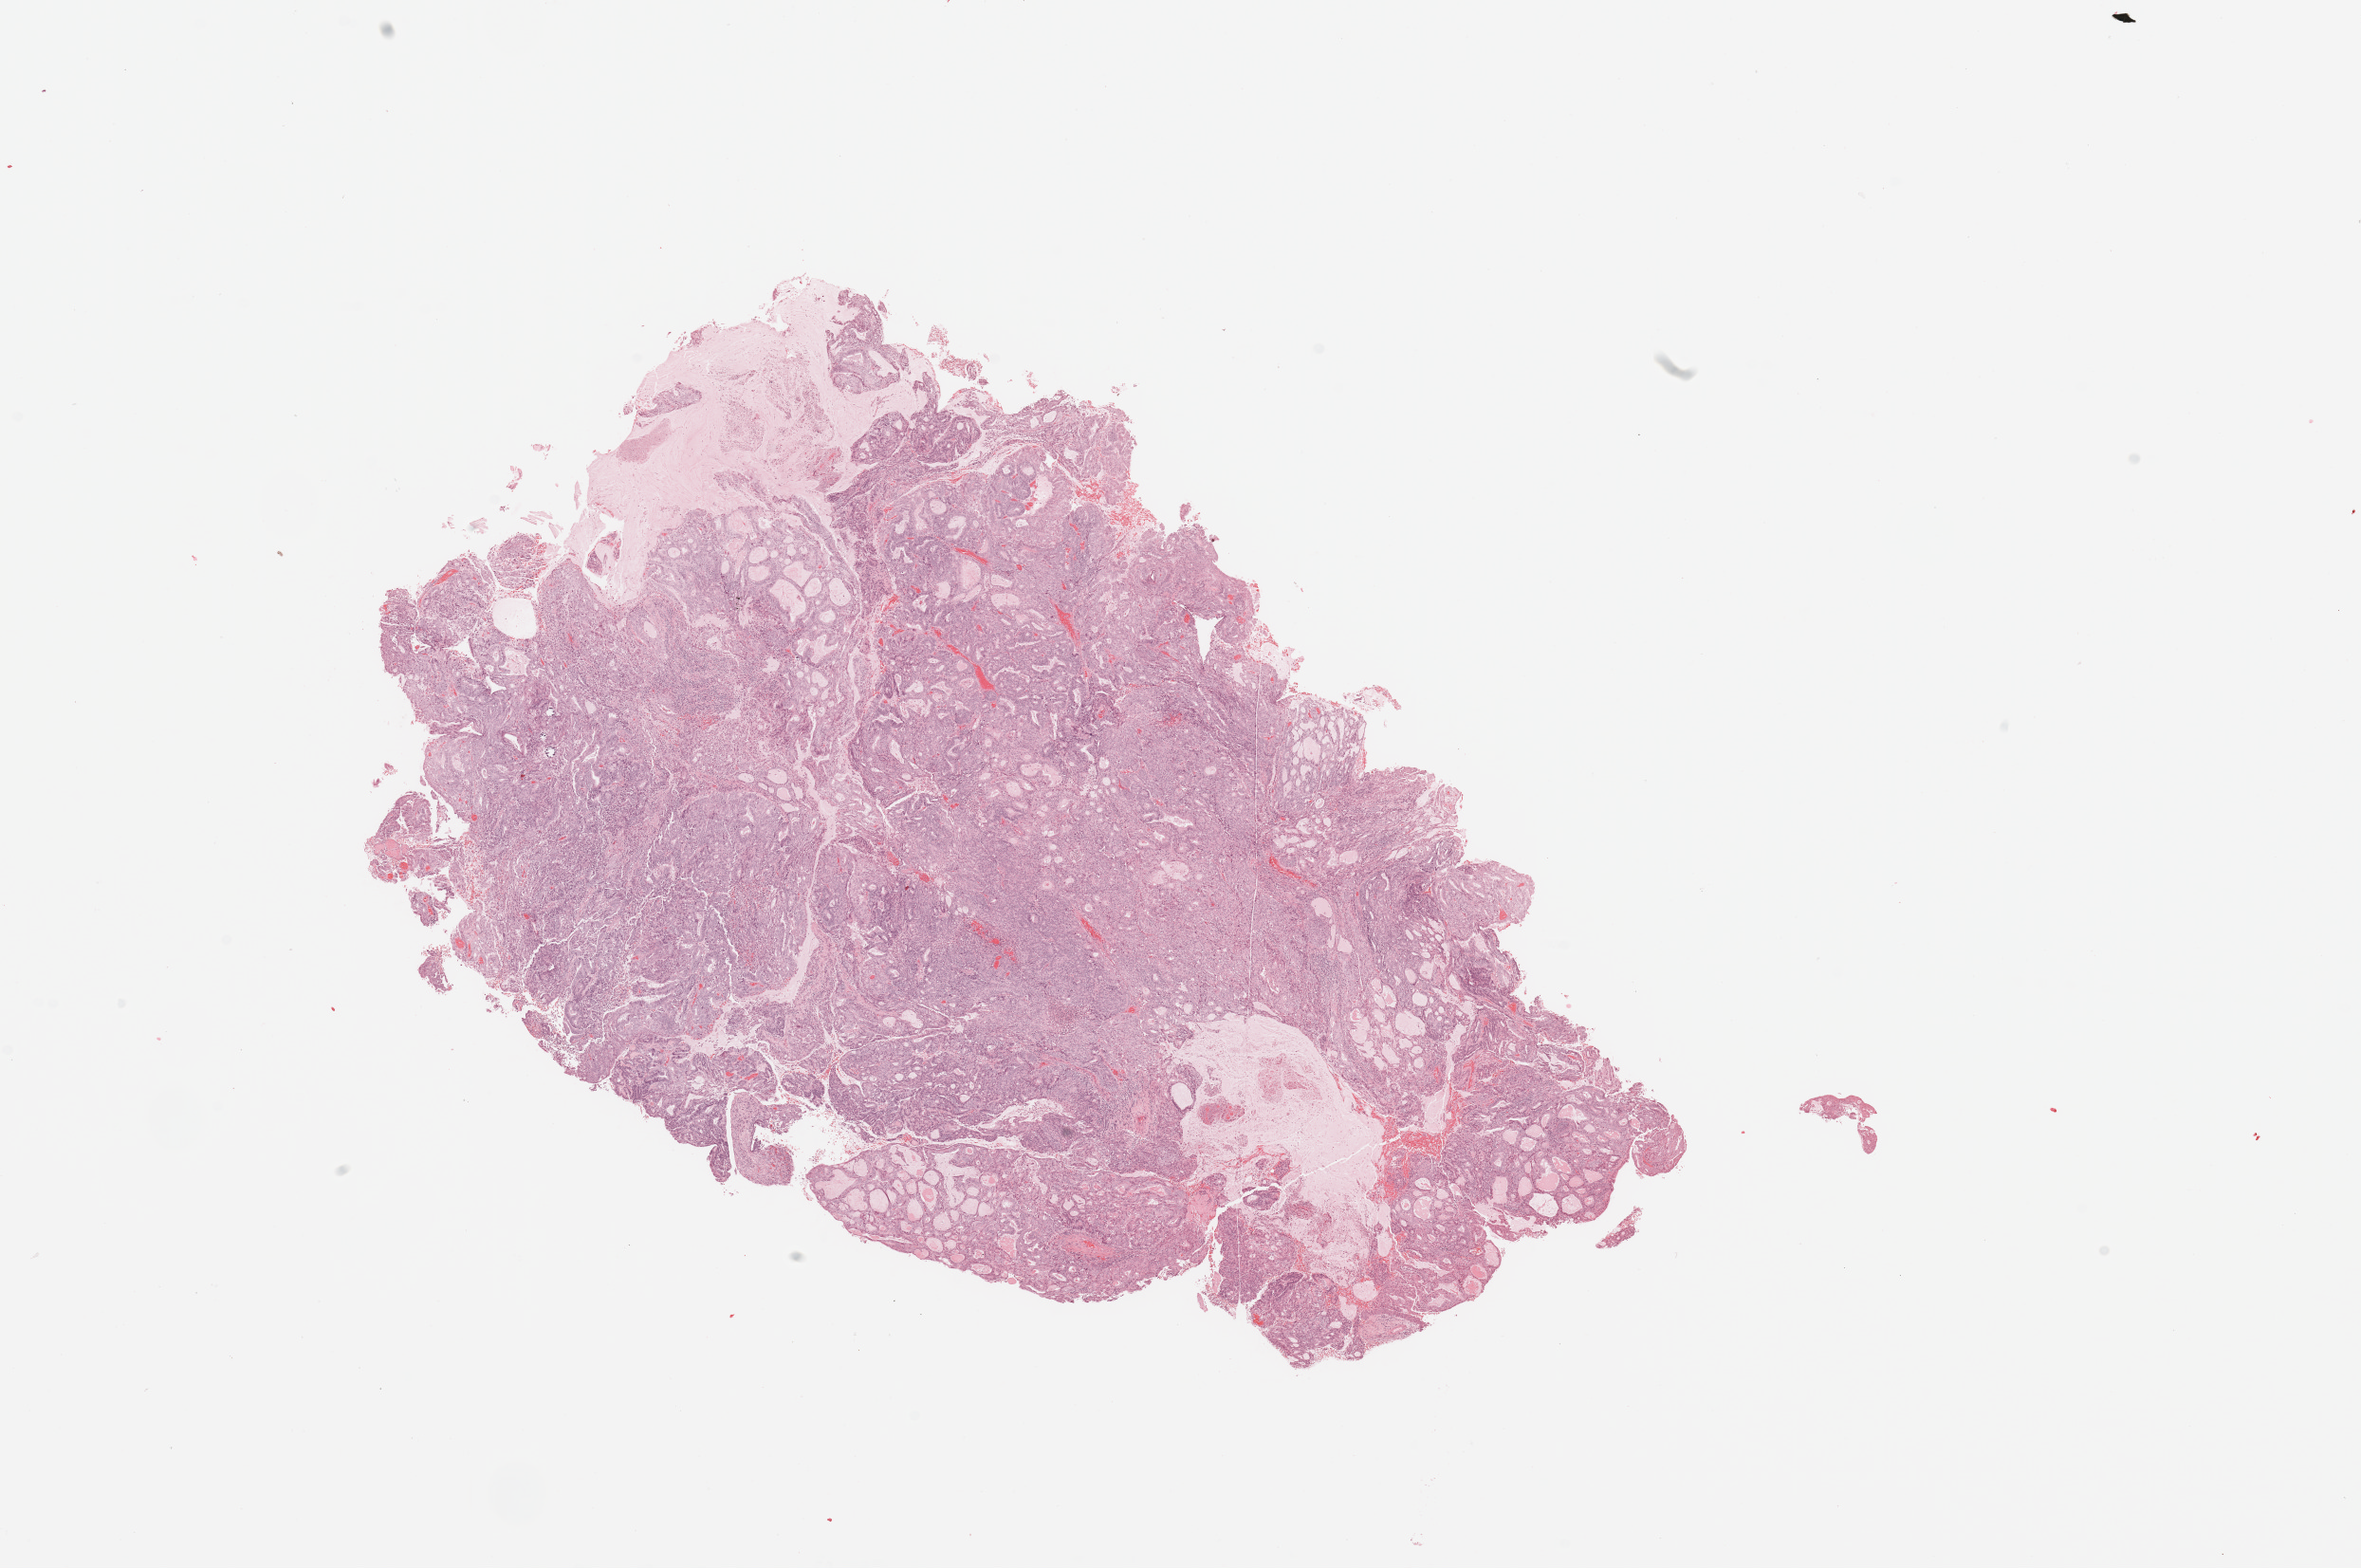
Whole-slide histology image, H&E-stained — whole scanned area (about 19.7 x 13.1 mm, acquisition: 20x scan) shown as a low-resolution overview. Tumour tissue sample, sampled site: uterus. Patient: female, age 66 years. Histologic grade: G2 (moderately differentiated). Pathologist review of this section (percent, as recorded): tumour nuclei 90%, necrosis 0%.
* AJCC pathologic stage: I
* histologic diagnosis: Endometrioid adenocarcinoma, NOS
* primary tumour site (as recorded): anterior endometrium